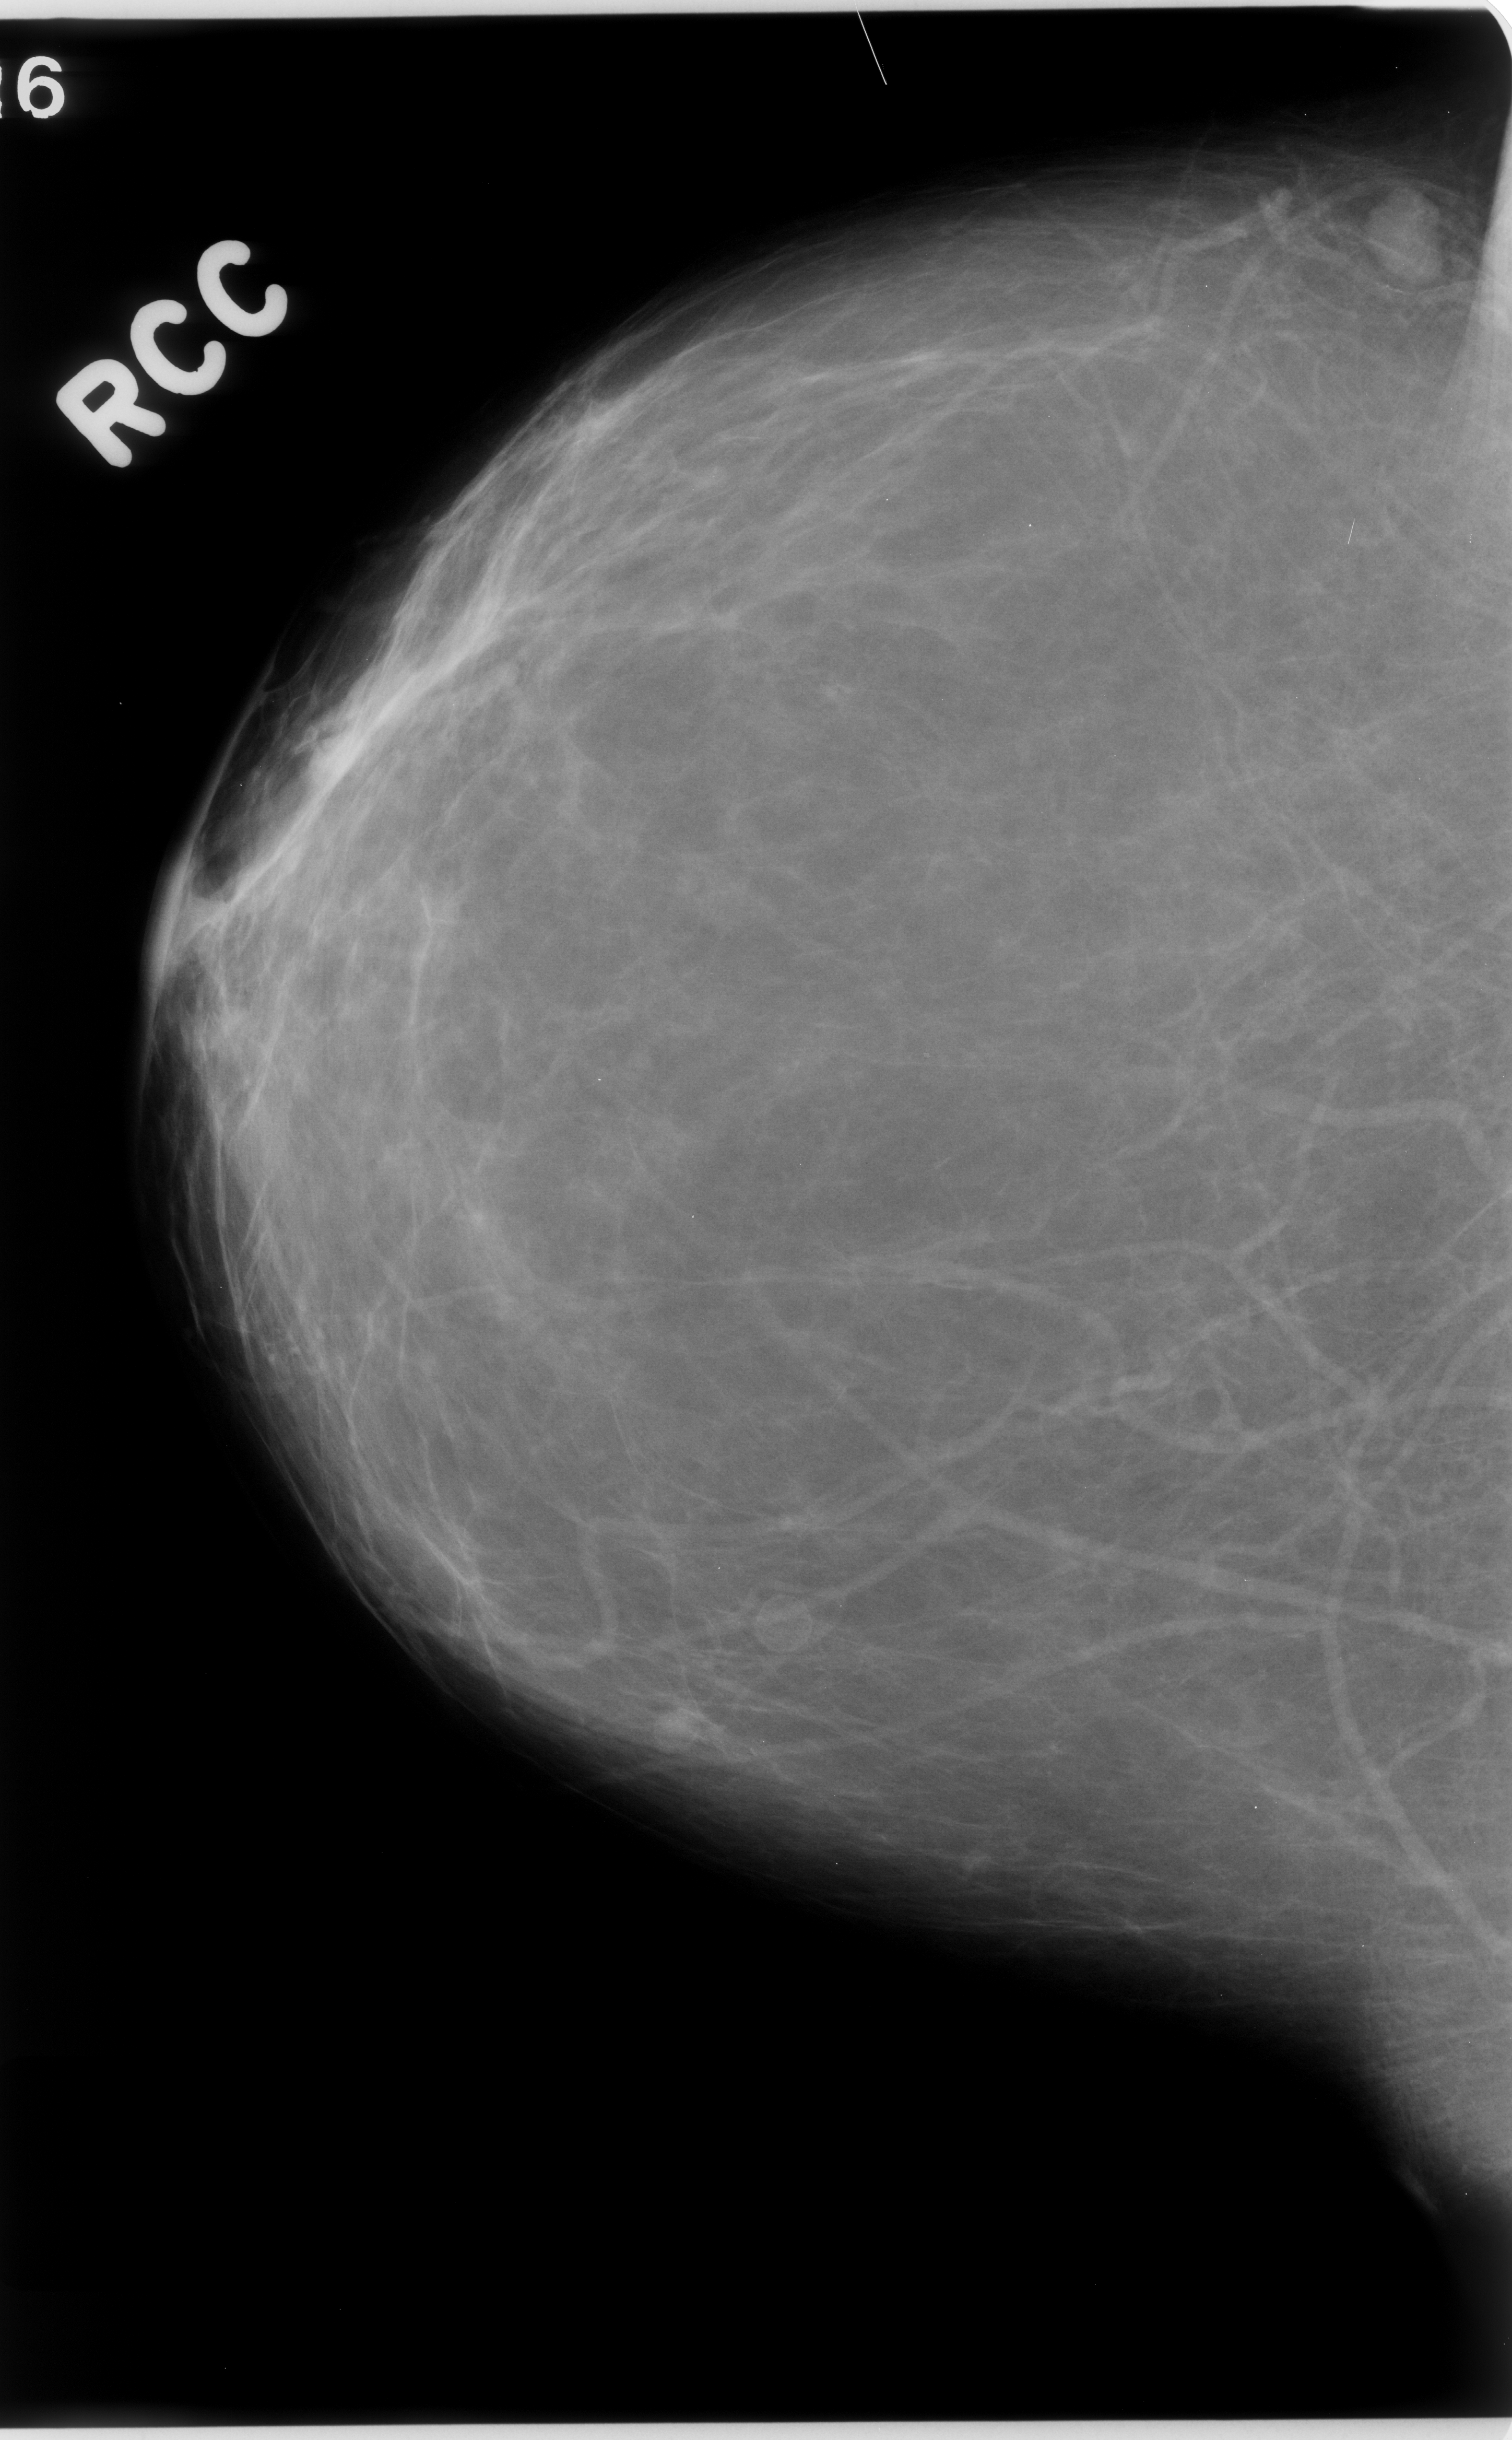
Scanned film-screen mammogram, right breast, craniocaudal (CC) view, breast composition: almost entirely fatty (BI-RADS density category 1 of 4).
Marked findings (only marked abnormalities are described; nothing is implied about the rest of the image): mass, shape oval, margins circumscribed; BI-RADS assessment category 3; subtlety rating 5 on a 1 (subtle) to 5 (obvious) scale; pathology (as recorded): benign.